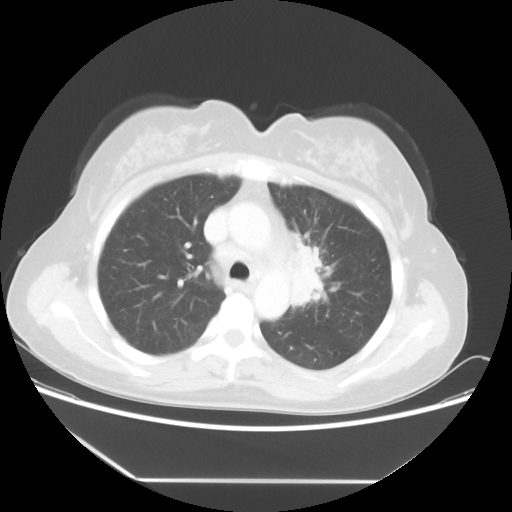
Chest CT, one axial slice; slice 36 of 52 in the series (ordered by position); reconstruction kernel STANDARD; 100 kVp; lung window (W 1500 / L -600 HU); 5 mm slice thickness; 512 × 512 image matrix, field of view 390 × 390 mm. Patient: female, 50 years. Case-level facts recorded for this patient, not image findings: clinical TNM (as recorded): T2 N3 M0.
Structures marked on this image (bounding box drawn by a radiologist):
- lung tumour (recorded histology: adenocarcinoma): box from (x=291, y=230) to (x=322, y=327) px